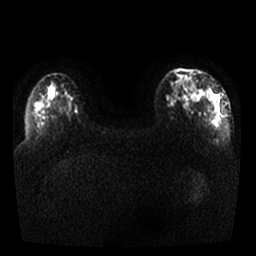
Breast MRI, one axial slice. Position 6 of 25 along the scan axis. Diffusion-weighted series; image 2 of 4 stored at this slice position (different b-values; order by instance number). 1.5 T. 256 × 256 image matrix, field of view 340 × 340 mm. Female patient.
Outlined on this slice (outlined manually by an expert reader):
- tumour on diffusion-weighted imaging: bounding box (x1, y1, x2, y2) in pixels: (190, 88, 221, 126)